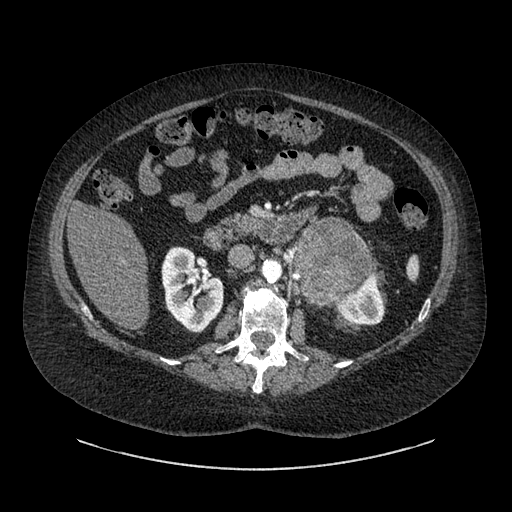
Contrast-enhanced abdominal CT, one axial slice. Slice 519 of 769 in the series (ordered by position). Soft-tissue window (W 400 / L 40 HU). 512 × 512 image matrix, field of view 460 × 460 mm. Female patient, age 61 years. From the clinical record (not read from this slice): diagnosis: adrenocortical carcinoma; tumour side: left adrenal; tumour size at pathology: 13 cm; Ki-67 index: 79 %; stage (as recorded): 2.
Outlined on this slice (semi-automatic segmentation, software-assisted and operator-edited):
- mass: bounding box [x1, y1, x2, y2] px = [299, 222, 369, 300]